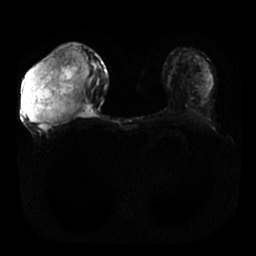
Breast MRI, one axial slice. Position 9 of 25 along the scan axis. Diffusion-weighted series; image 2 of 4 stored at this slice position (different b-values; order by instance number). 1.5 T. 4 mm slice thickness. 256 × 256 image matrix, field of view 340 × 340 mm. Female patient.
Structures marked on this image (expert manual segmentation):
- tumour on diffusion-weighted imaging: bounding box (x1, y1, x2, y2) in pixels: (24, 46, 89, 124)